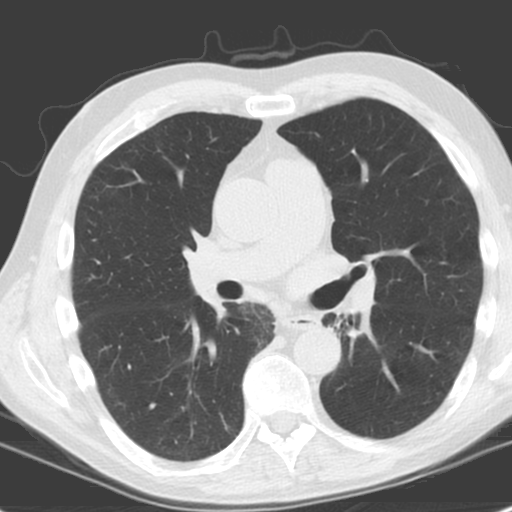
Low-dose screening chest CT, axial slice; baseline screening round; lung window (W 1500 / L -600 HU); 3.2 mm slice thickness; standard (soft-tissue) reconstruction kernel (C); 120 kVp; slice 83 of 185 in the series; 512 × 512 image matrix. Male, age 61 years at enrolment. Former smoker at enrolment.
Expert-annotated lung lesion, bounding box (x1, y1, x2, y2) in pixels: (313, 309, 363, 344). No non-calcified nodule or mass ≥4 mm was recorded by the screening reader at this exam.